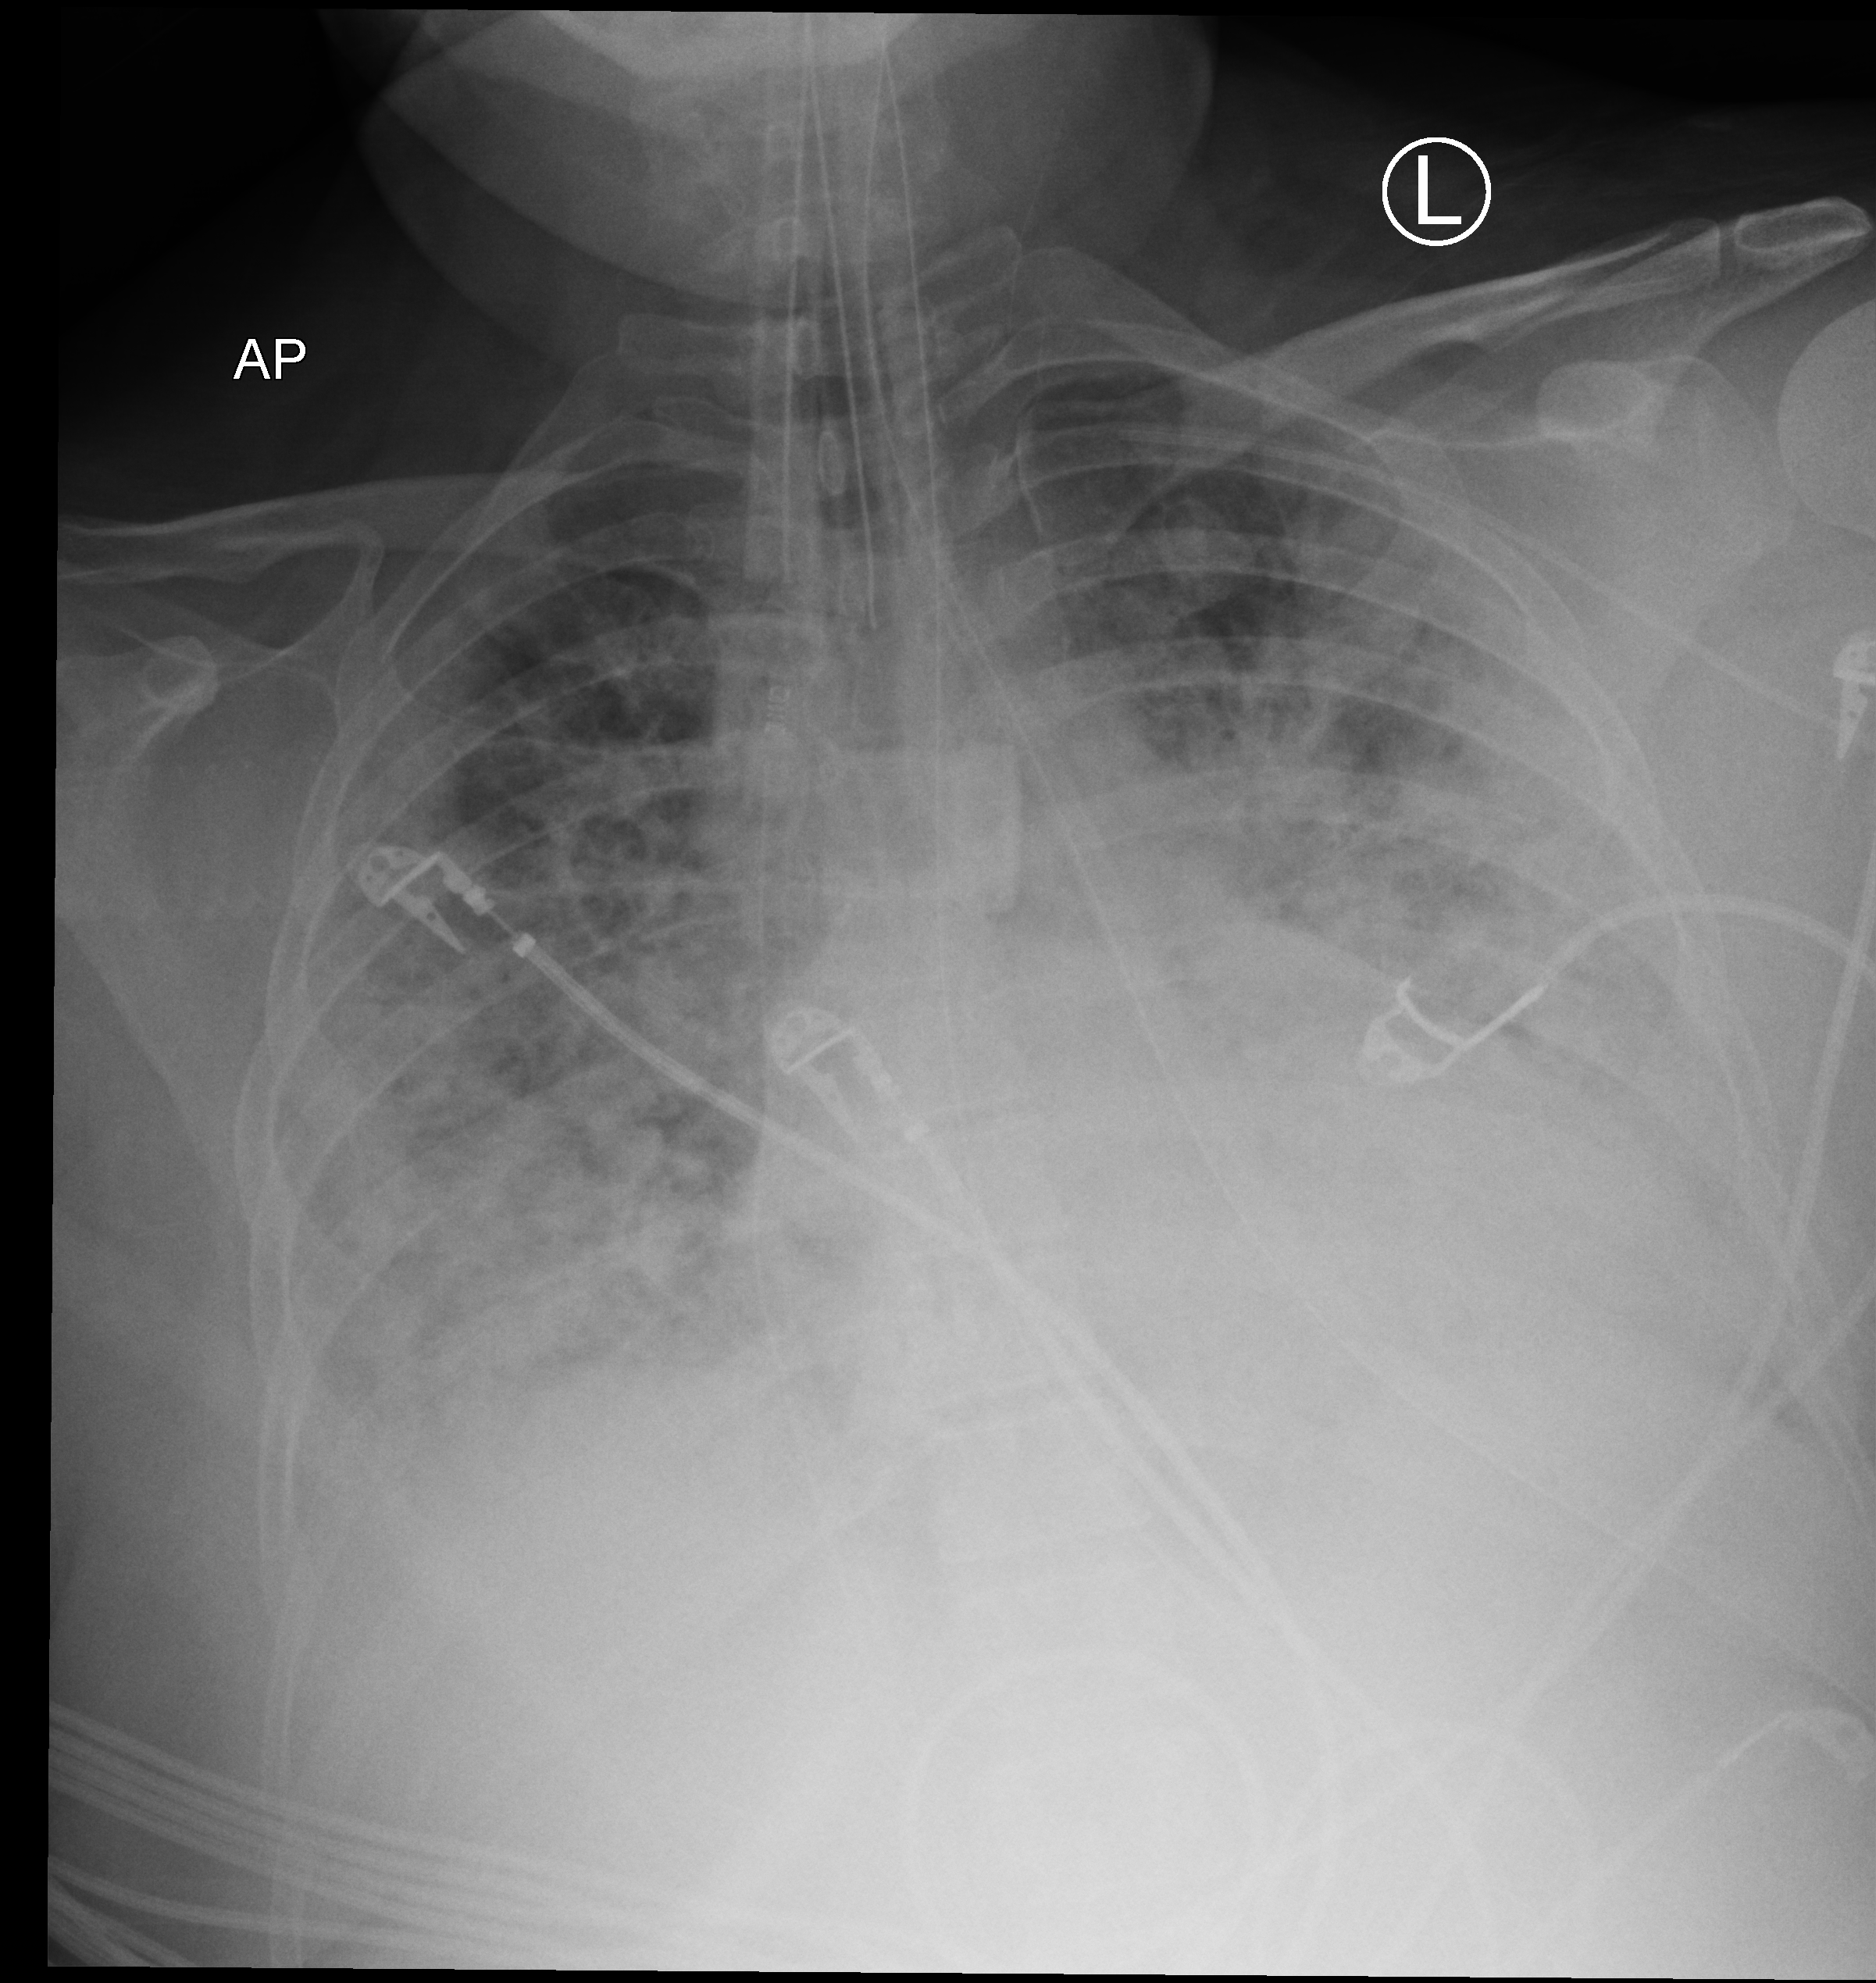
Chest X-ray (portable); anteroposterior (AP) projection. Patient hospitalised with COVID-19; female, aged 18–59 years.
From the hospital-stay record, not from the radiograph (when in the stay this image was taken is not recorded): admitted to intensive care during this hospital stay: yes; mechanically ventilated during this hospital stay: yes.